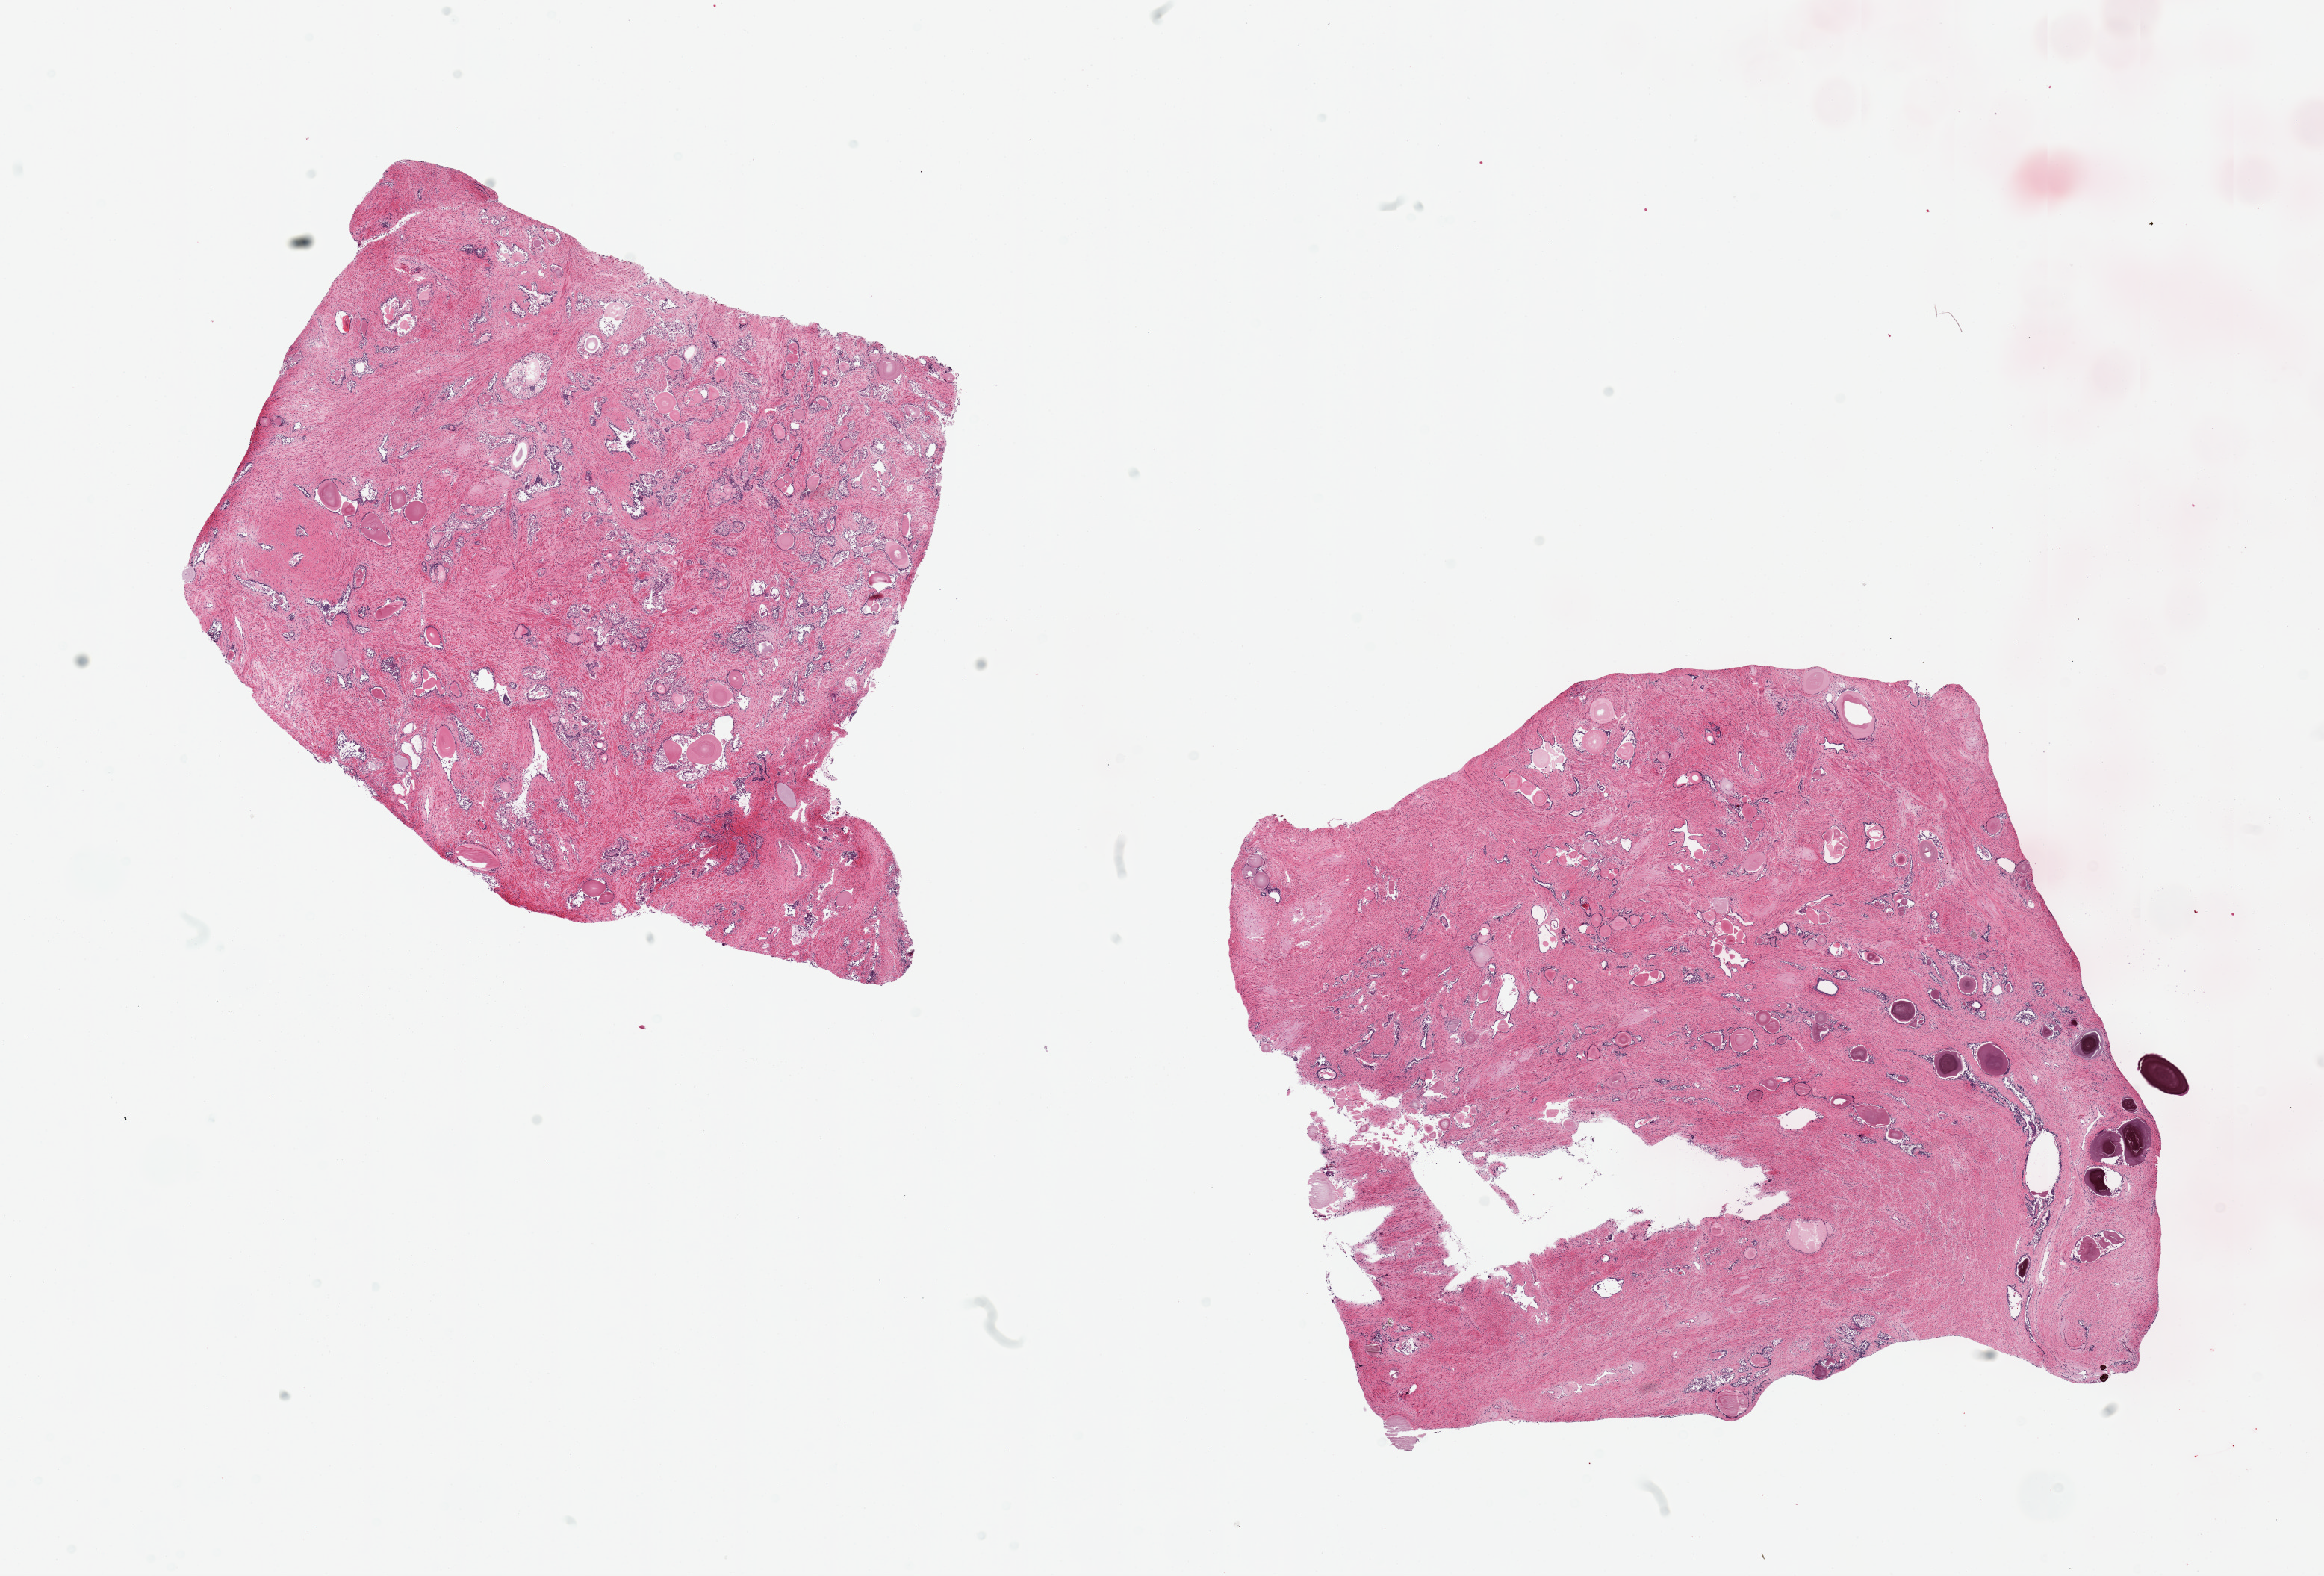
Digitized H&E-stained section, brightfield — shown as a low-resolution overview of the whole scanned area (about 24.6 x 16.7 mm). PAXgene-fixed, paraffin-embedded tissue. Sampled site (target tissue): prostate. Tissue donor sample. Male donor.
* review note (as recorded): 2 pieces, moderate-severe glandular autolysis